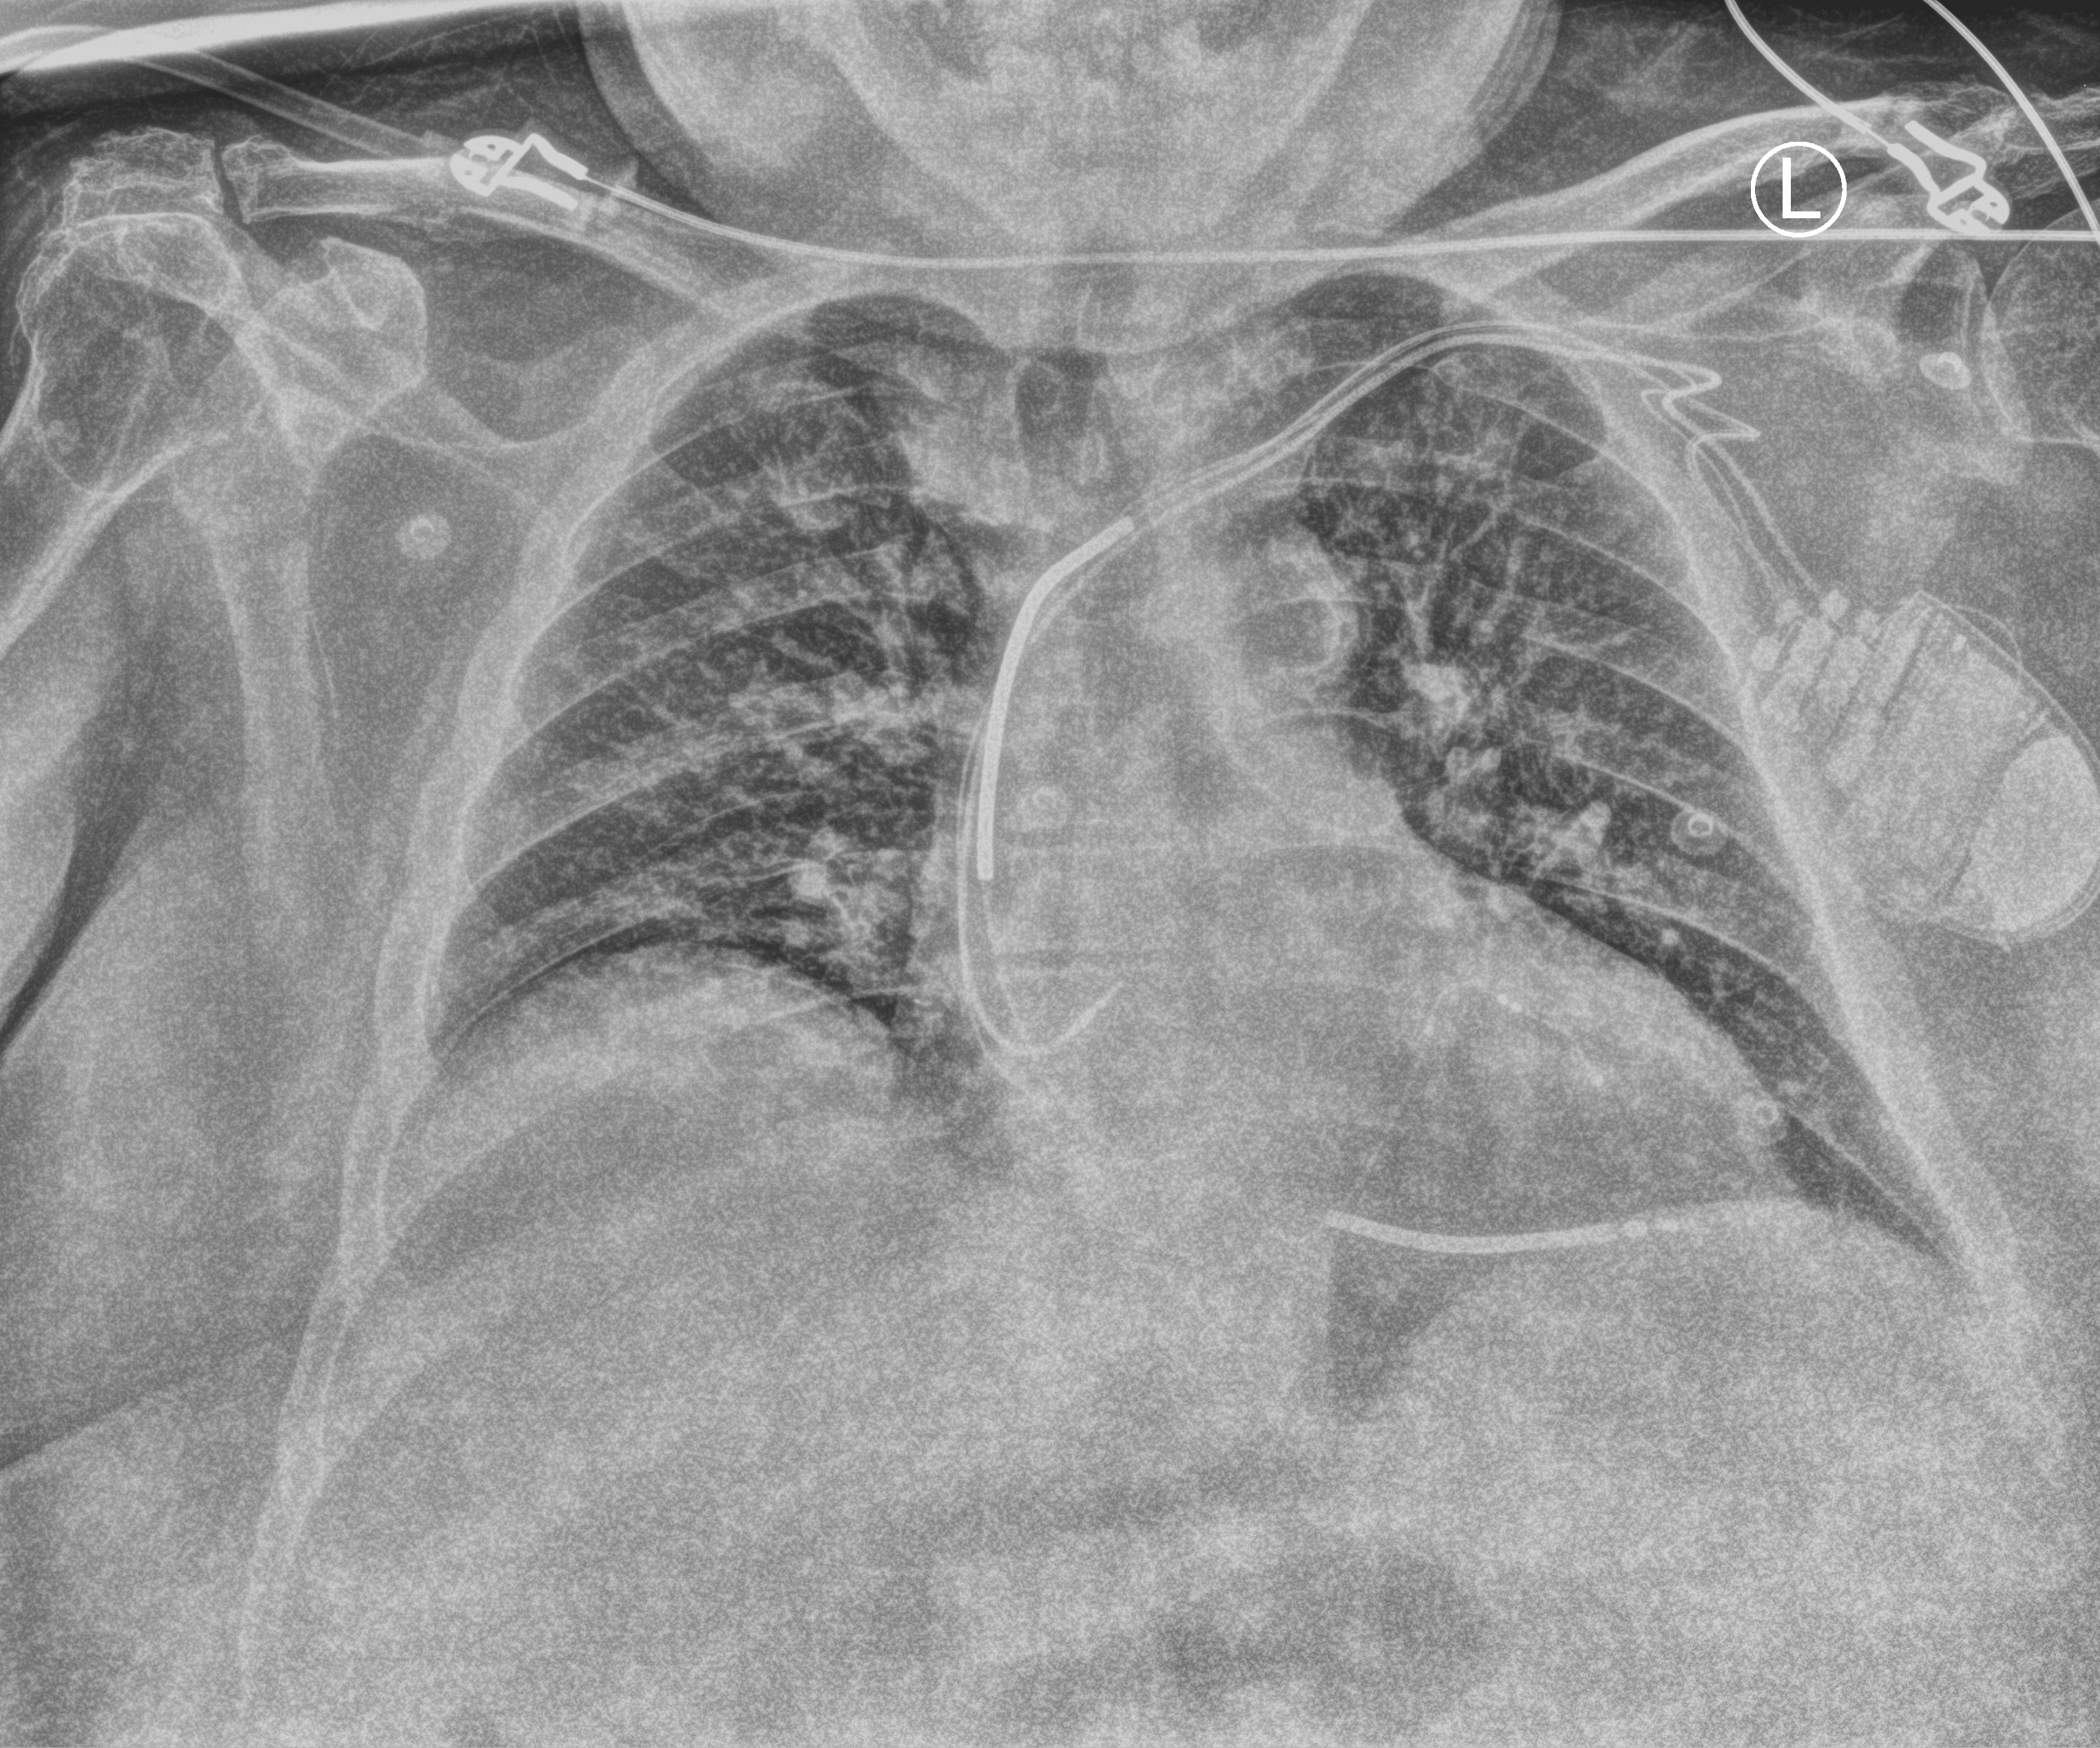
Chest X-ray (portable); anteroposterior (AP) projection. Patient hospitalised with COVID-19; male, aged 75–90 years.
Hospital-stay facts (about this admission, not read from this image; timing relative to this image not recorded):
- admitted to intensive care during this hospital stay: no
- mechanically ventilated during this hospital stay: no